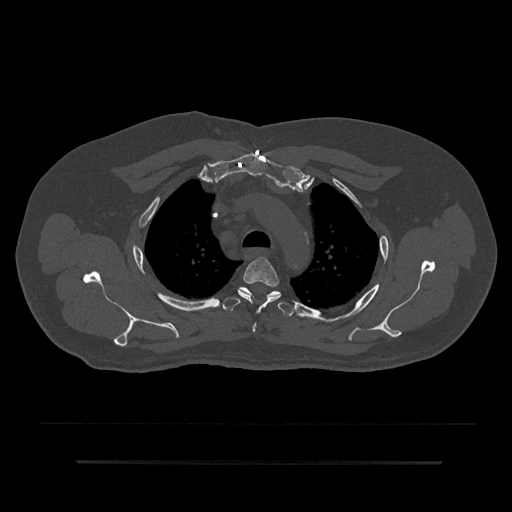
CT including the spine, one axial slice; position 644 of 797 along the scan axis; reconstruction kernel Br40s/3; 120 kVp; bone window (W 1800 / L 400 HU); 512 × 512 image matrix, field of view 464 × 464 mm. Patient: male, 59 years. From the clinical record (not read from this slice): primary cancer: bile ducts.
Annotated regions visible in this slice (semi-automatic segmentation, software-assisted and operator-edited):
- T3 vertebra: bounding box (x1, y1, x2, y2) in pixels: (238, 257, 281, 332)
- T4 vertebra: (222, 287, 294, 316)